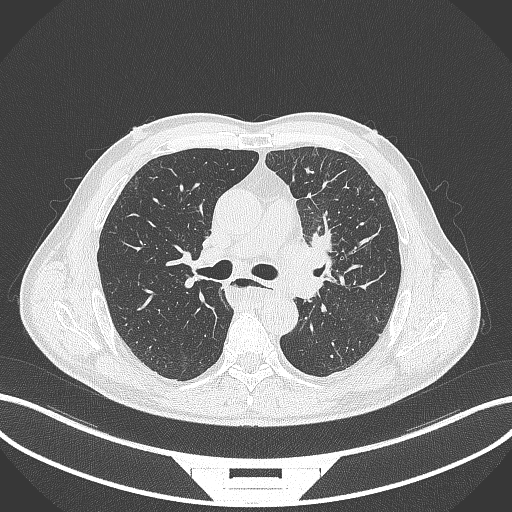
Chest CT, one axial slice; slice 233 of 411 in the series (ordered by position); reconstruction kernel B70f; lung window (W 1500 / L -600 HU); 1 mm slice thickness; 512 × 512 image matrix, field of view 400 × 400 mm. Patient: male, 57 years. Case-level facts recorded for this patient, not image findings: clinical TNM (as recorded): T2a N1 M0.
Structures marked on this image (bounding box drawn by a radiologist):
- lung tumour (recorded histology: squamous cell carcinoma): box from (x=273, y=229) to (x=342, y=306) px